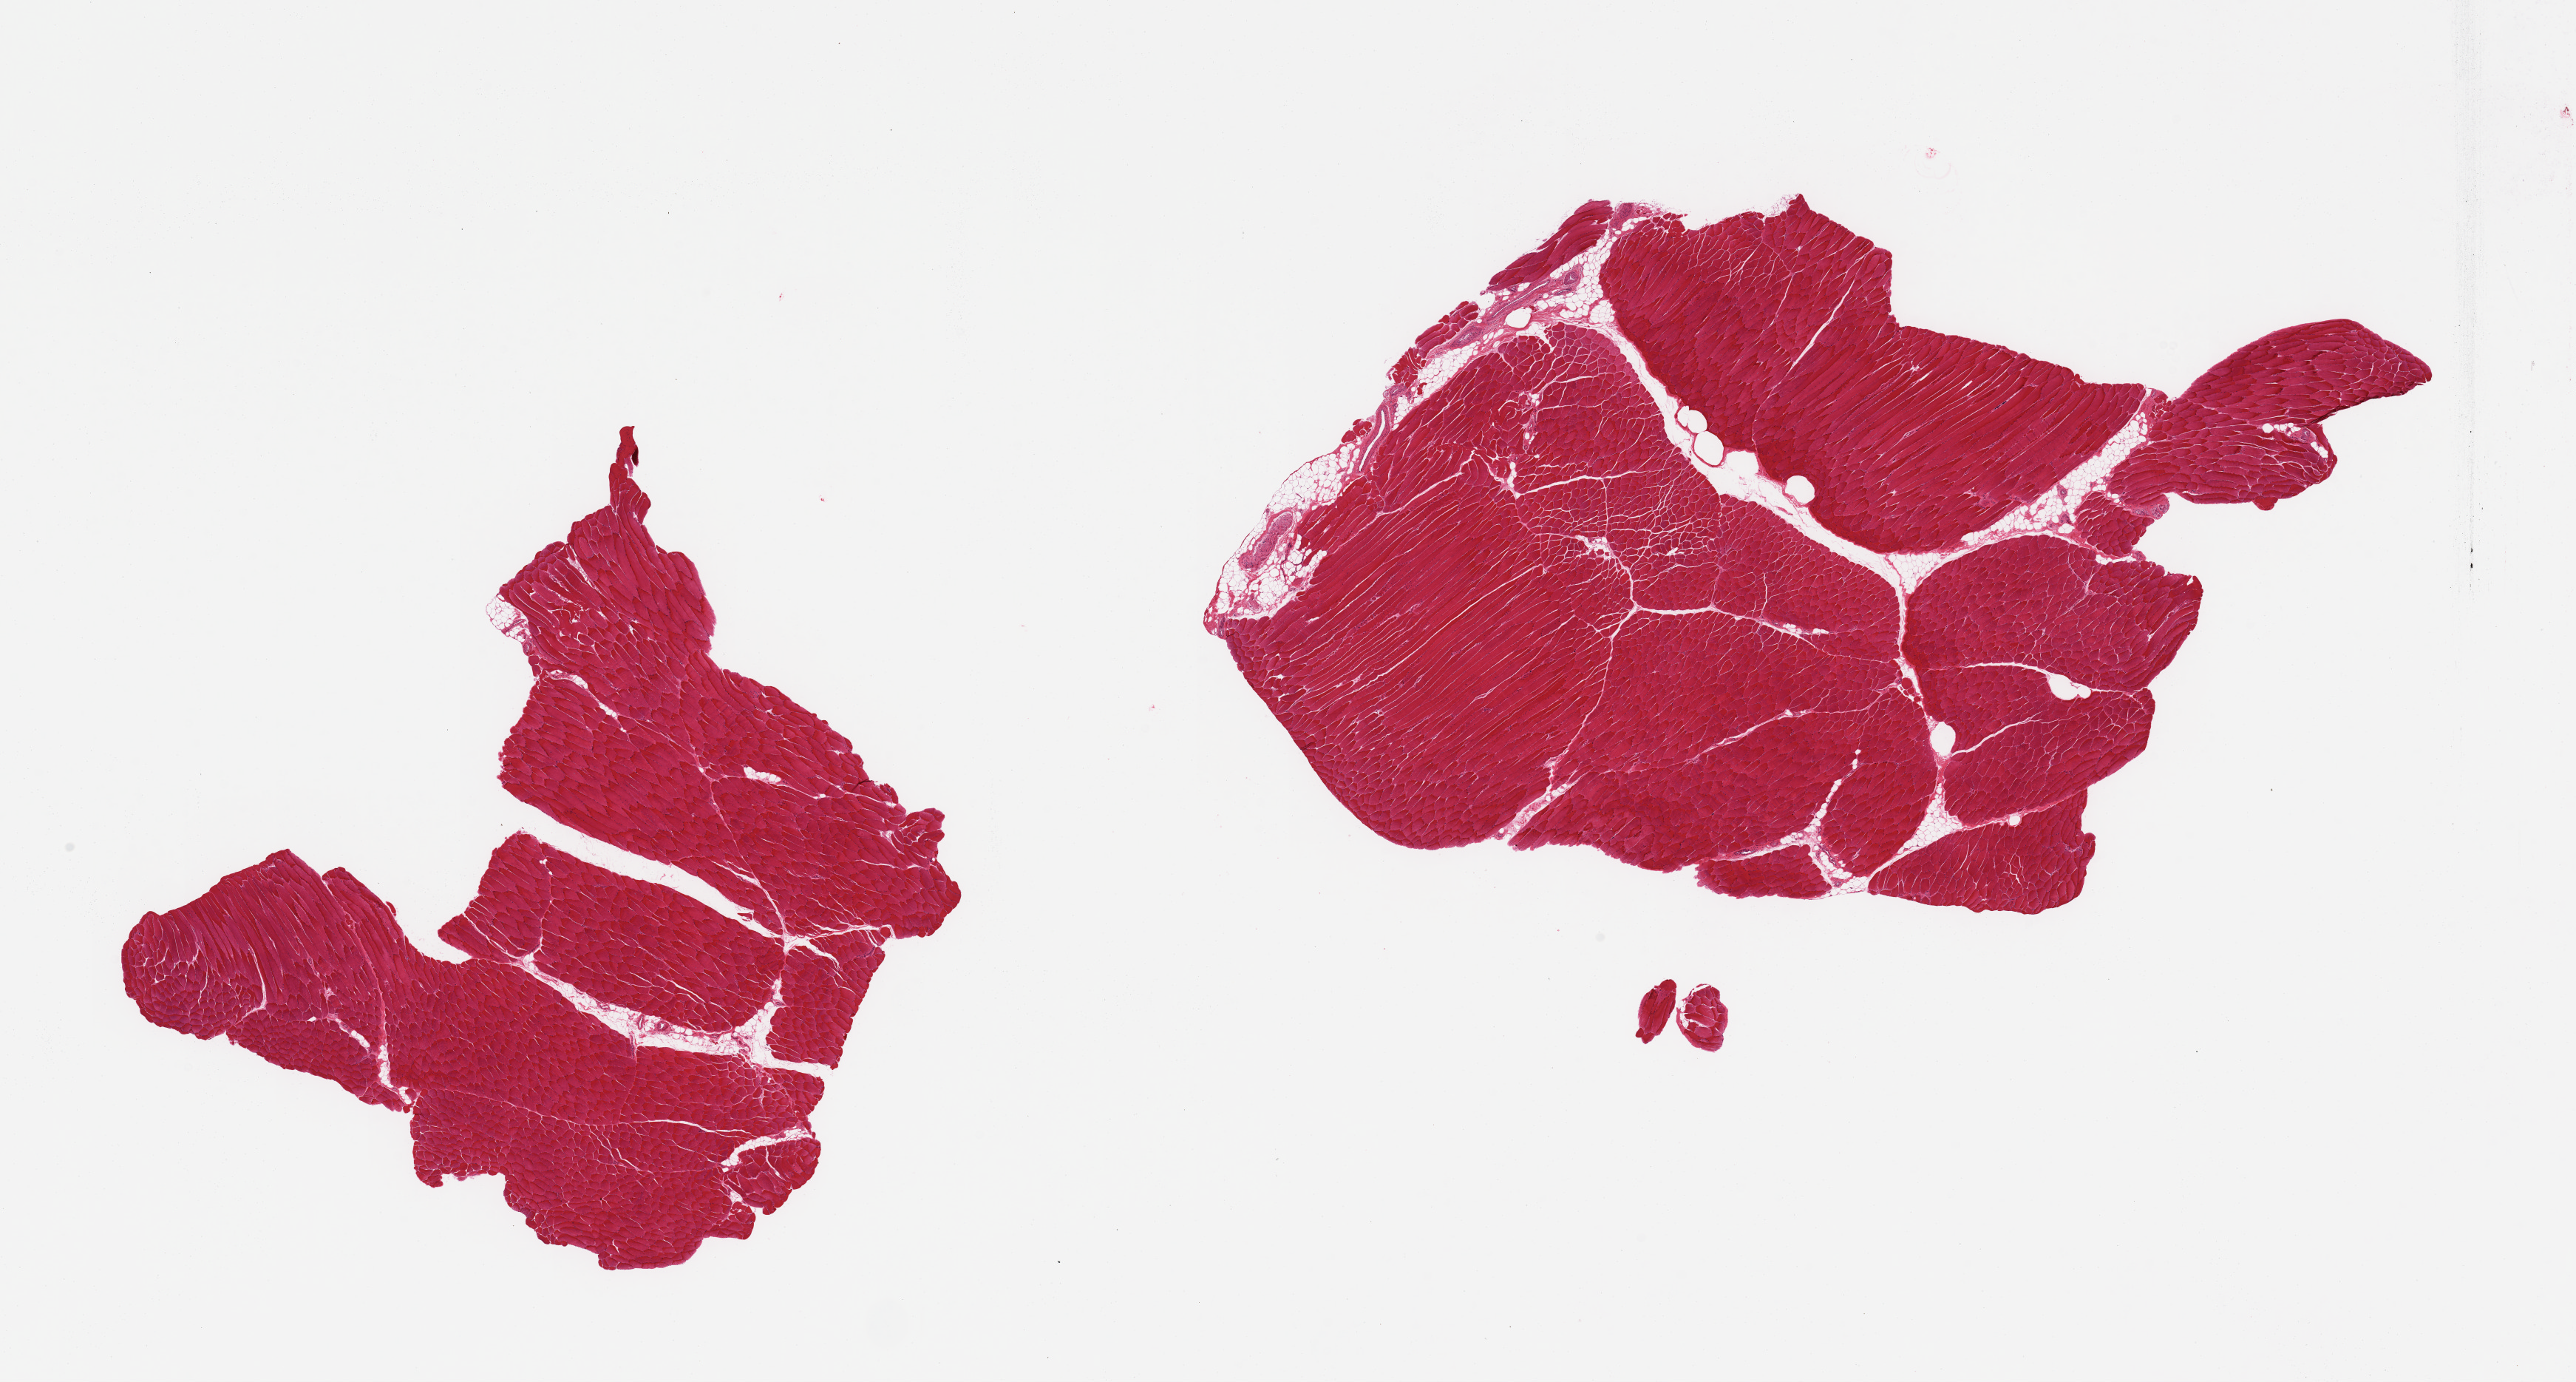
Digitized haematoxylin and eosin-stained section — low-resolution overview of the scanned area, about 27.6 x 14.8 mm (acquisition: 20x scan). PAXgene-fixed, paraffin-embedded tissue. Section of skeletal muscle (target tissue). Tissue donor sample.
Reviewer comment on this tissue sample: 2 pieces; skeletal muscle with <10% internal fat.